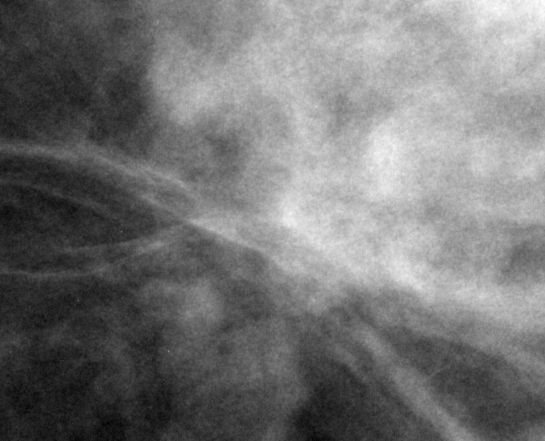
Crop from a digitized film mammogram around one marked abnormality; right breast; CC view; BI-RADS breast density category 3 (scale 1–4).
Finding: mass, shape architectural distortion, margins spiculated; BI-RADS assessment category 5; subtlety rating 1 on a 1 (subtle) to 5 (obvious) scale; pathology result (as recorded, not read from the image): malignant.